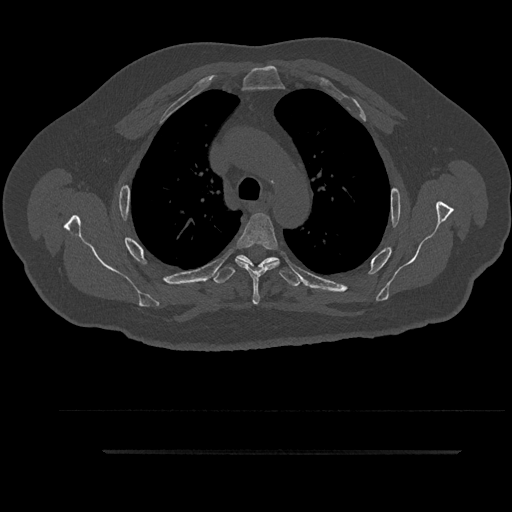
CT including the spine, one axial slice; slice 659 of 797 in the series (ordered by position); reconstruction kernel Br40s/3; 120 kVp; bone window (W 1800 / L 400 HU); 0.5 mm slice thickness; 512 × 512 image matrix, field of view 432 × 432 mm. Patient: male, 63 years. Case-level facts recorded for this patient, not image findings: primary cancer: renal; vertebrae with lytic lesions (as recorded): T8.
Structures marked on this image (semi-automatic segmentation, software-assisted and operator-edited):
- T3 vertebra: bounding box (x1, y1, x2, y2) in pixels: (224, 260, 299, 282)
- T4 vertebra: (236, 214, 280, 305)
- T5 vertebra: (213, 255, 300, 287)